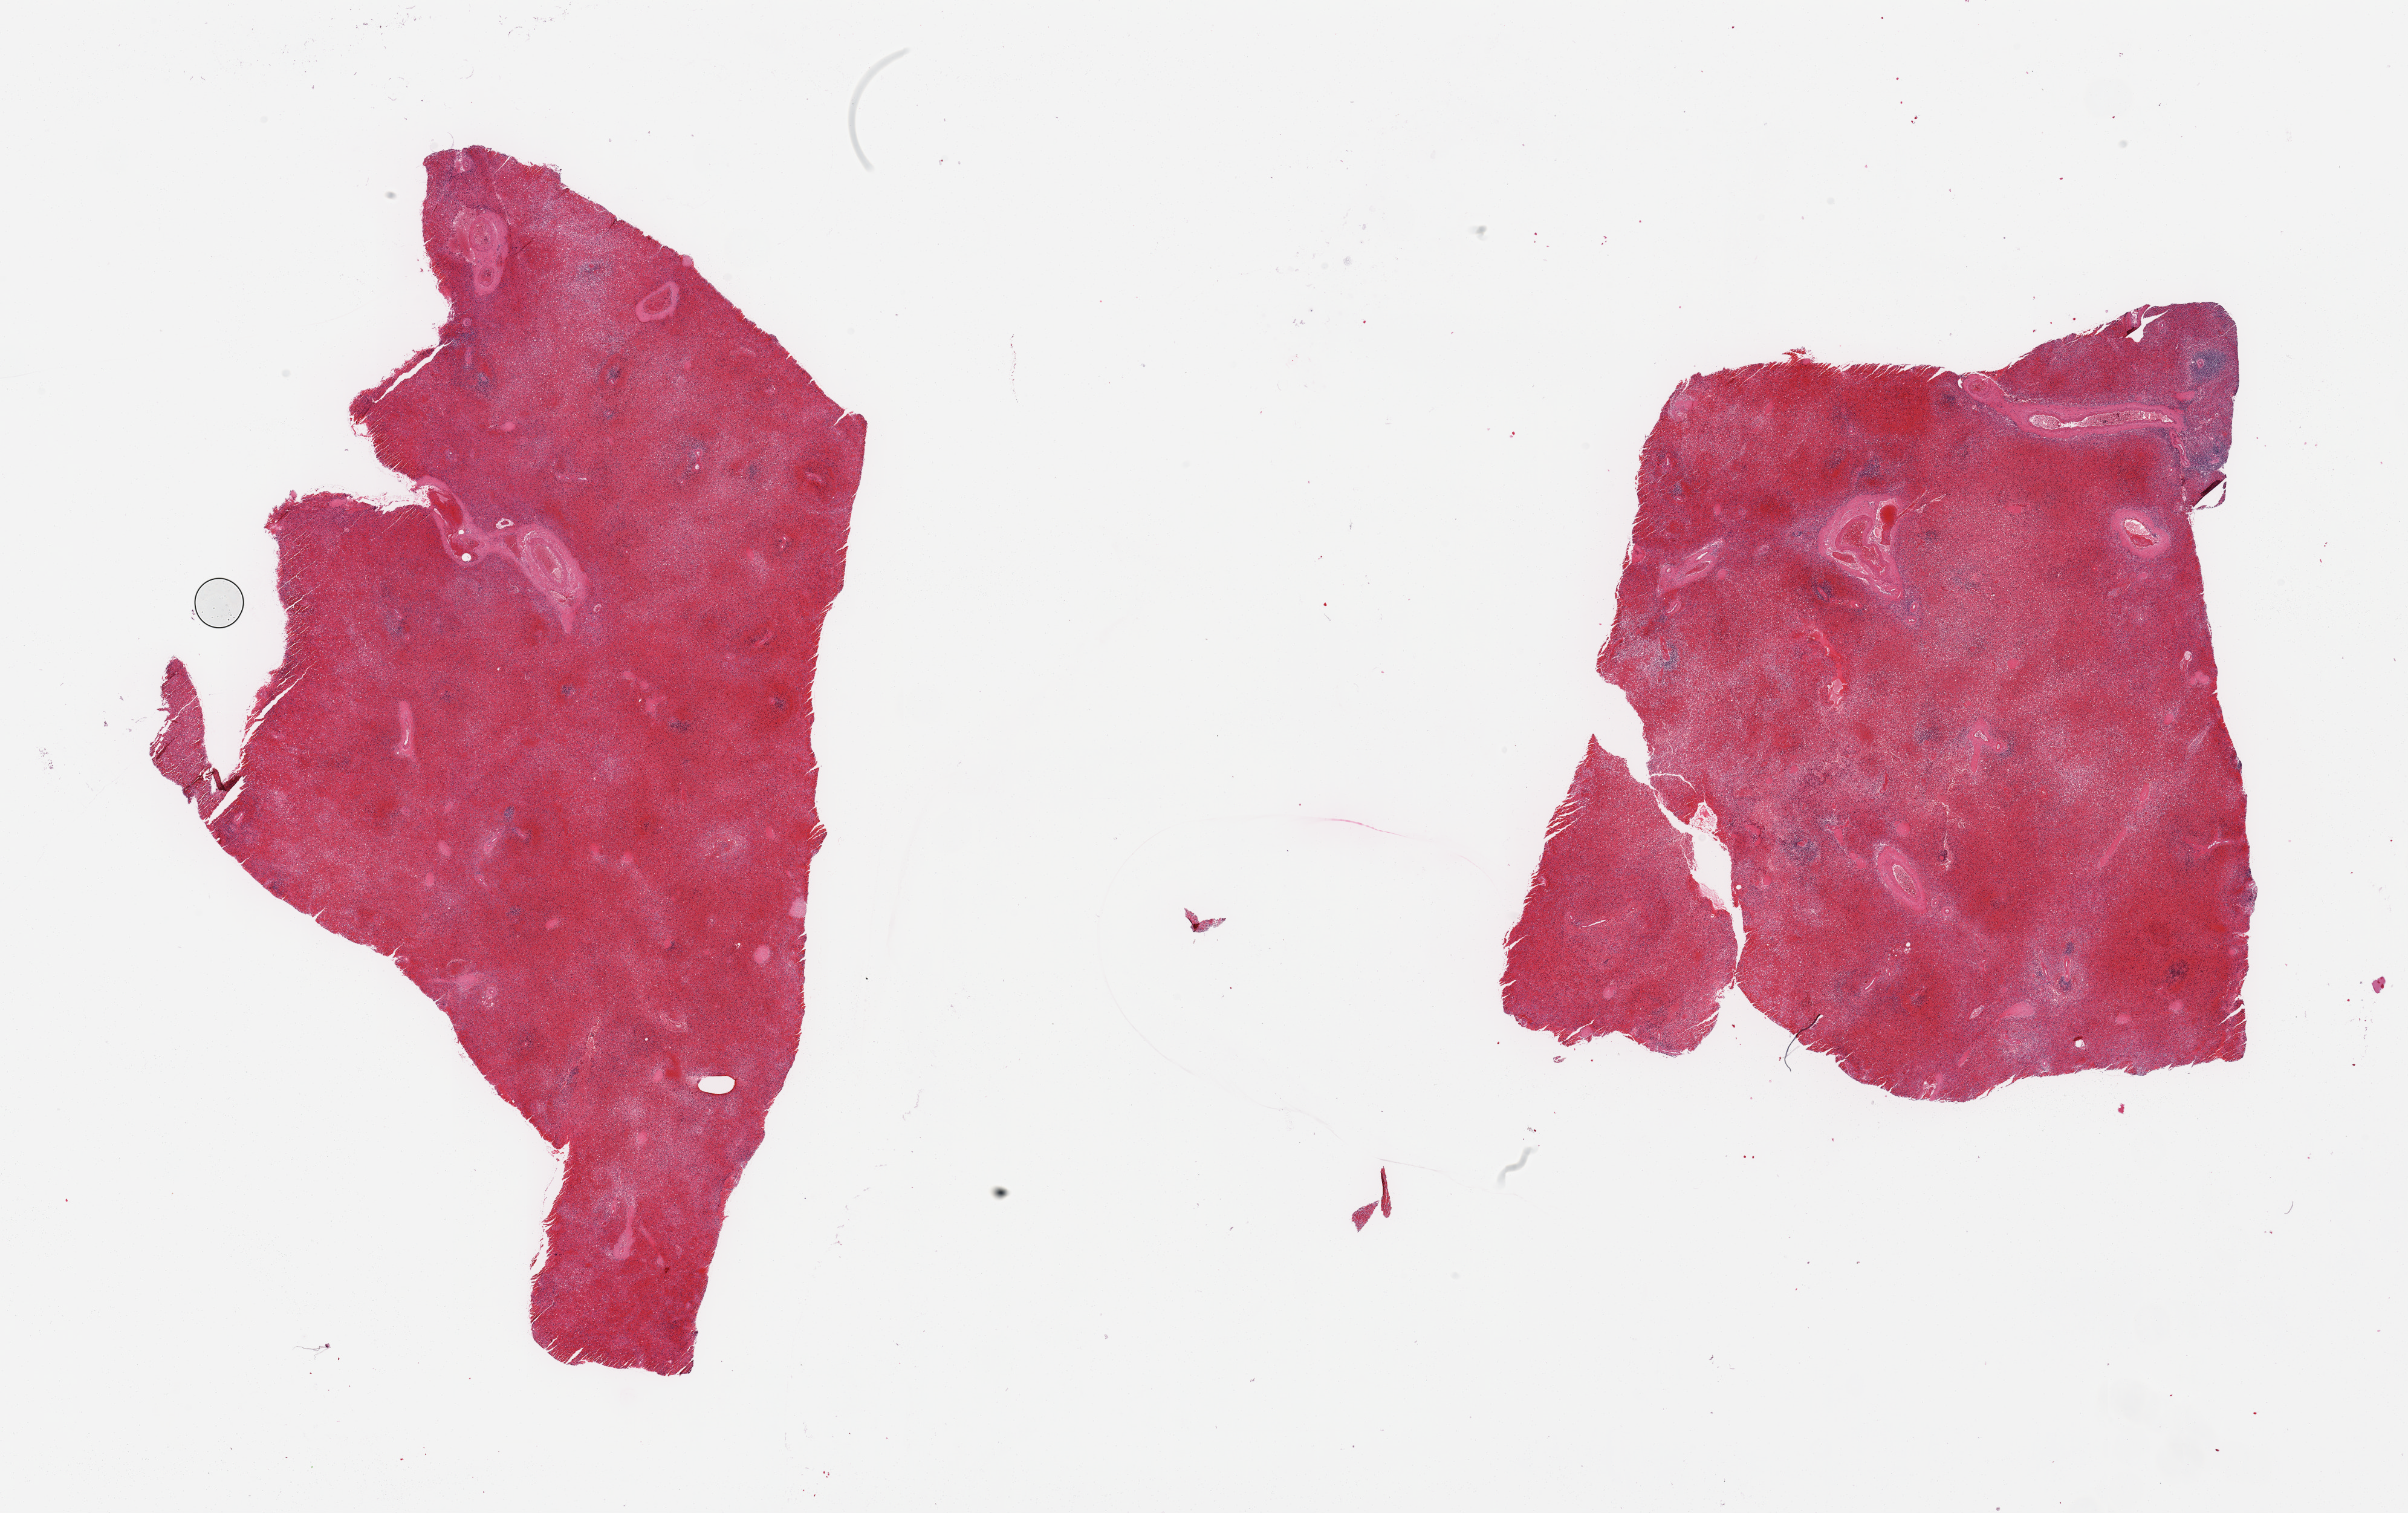
H&E whole-slide image, shown as a low-resolution overview of the whole scanned area (about 31.5 x 19.8 mm); PAXgene-fixed paraffin-embedded (PFPE) section; section of spleen (target tissue); tissue donor sample. Male donor.
Review note (as recorded): 2 pieces; moderately congested.